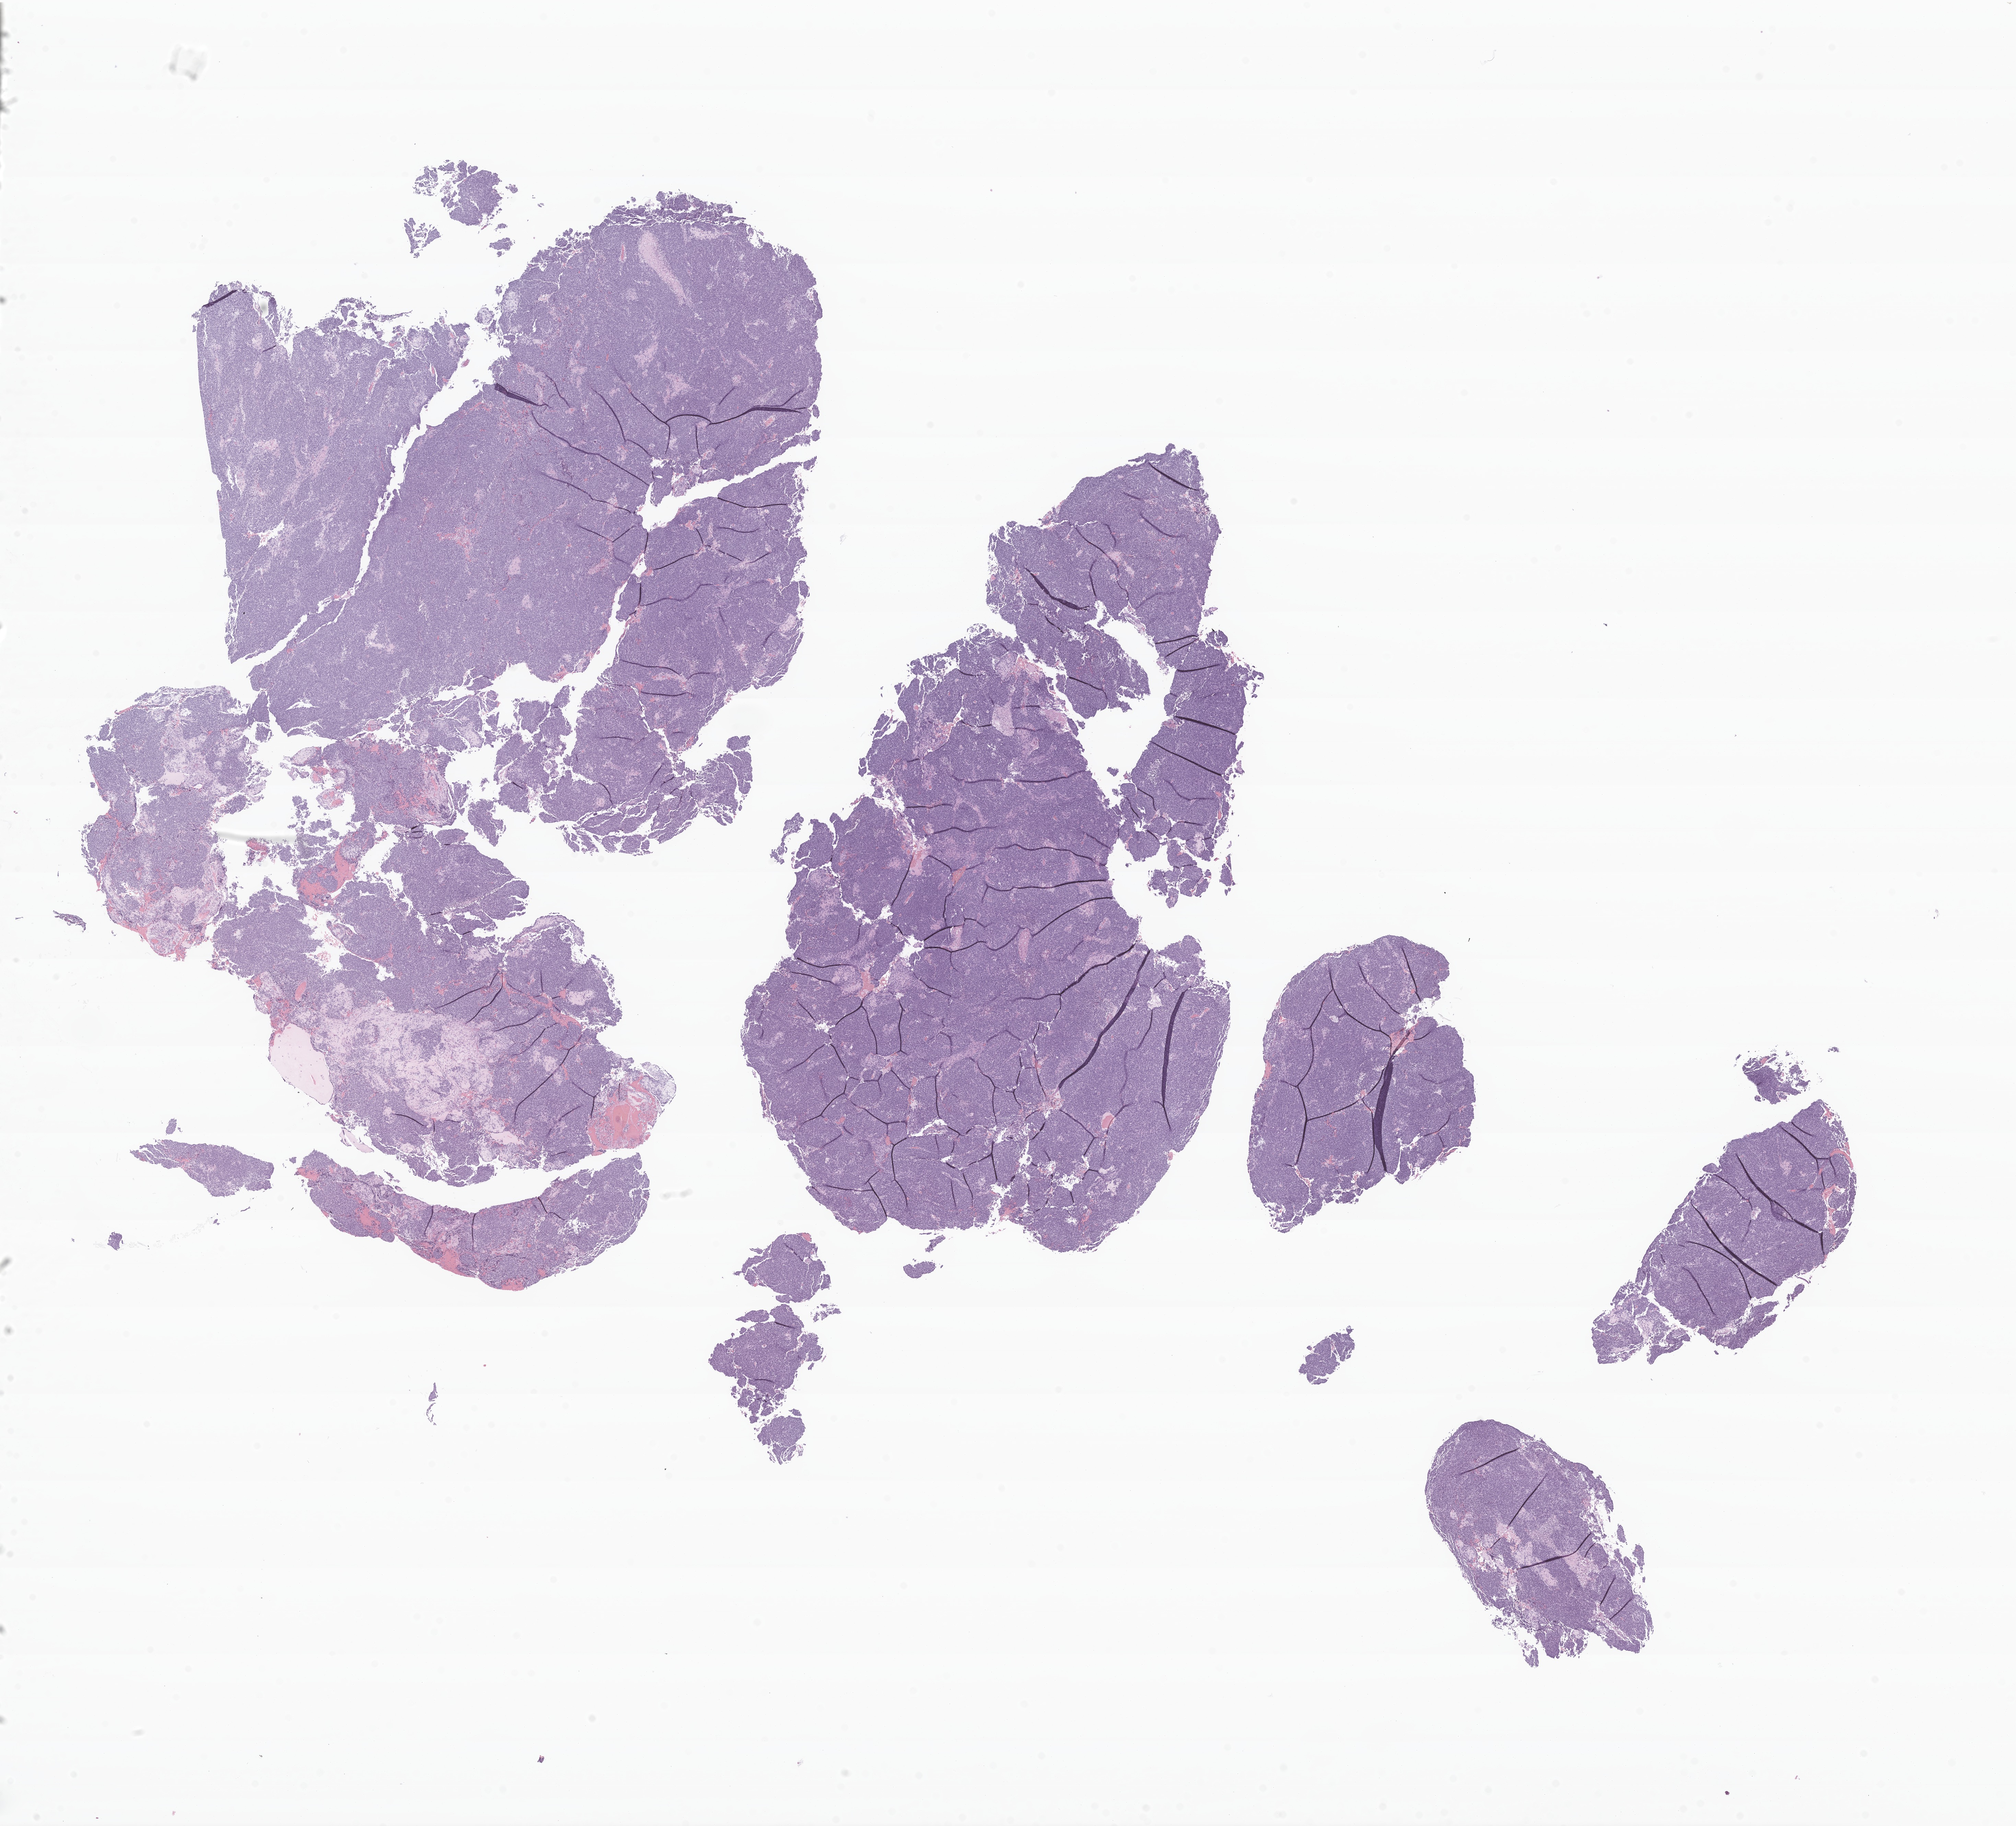
Whole-slide image, hematoxylin and eosin (H&E) stain of tumor tissue from the brain — whole scanned area (about 24.7 x 22.4 mm) shown as a low-resolution overview, formalin-fixed, paraffin-embedded (FFPE) tissue. Patient male; age 282 months (23 years 6 months).
* diagnosis (ICD-O-3 morphology term): Medulloblastoma, NOS